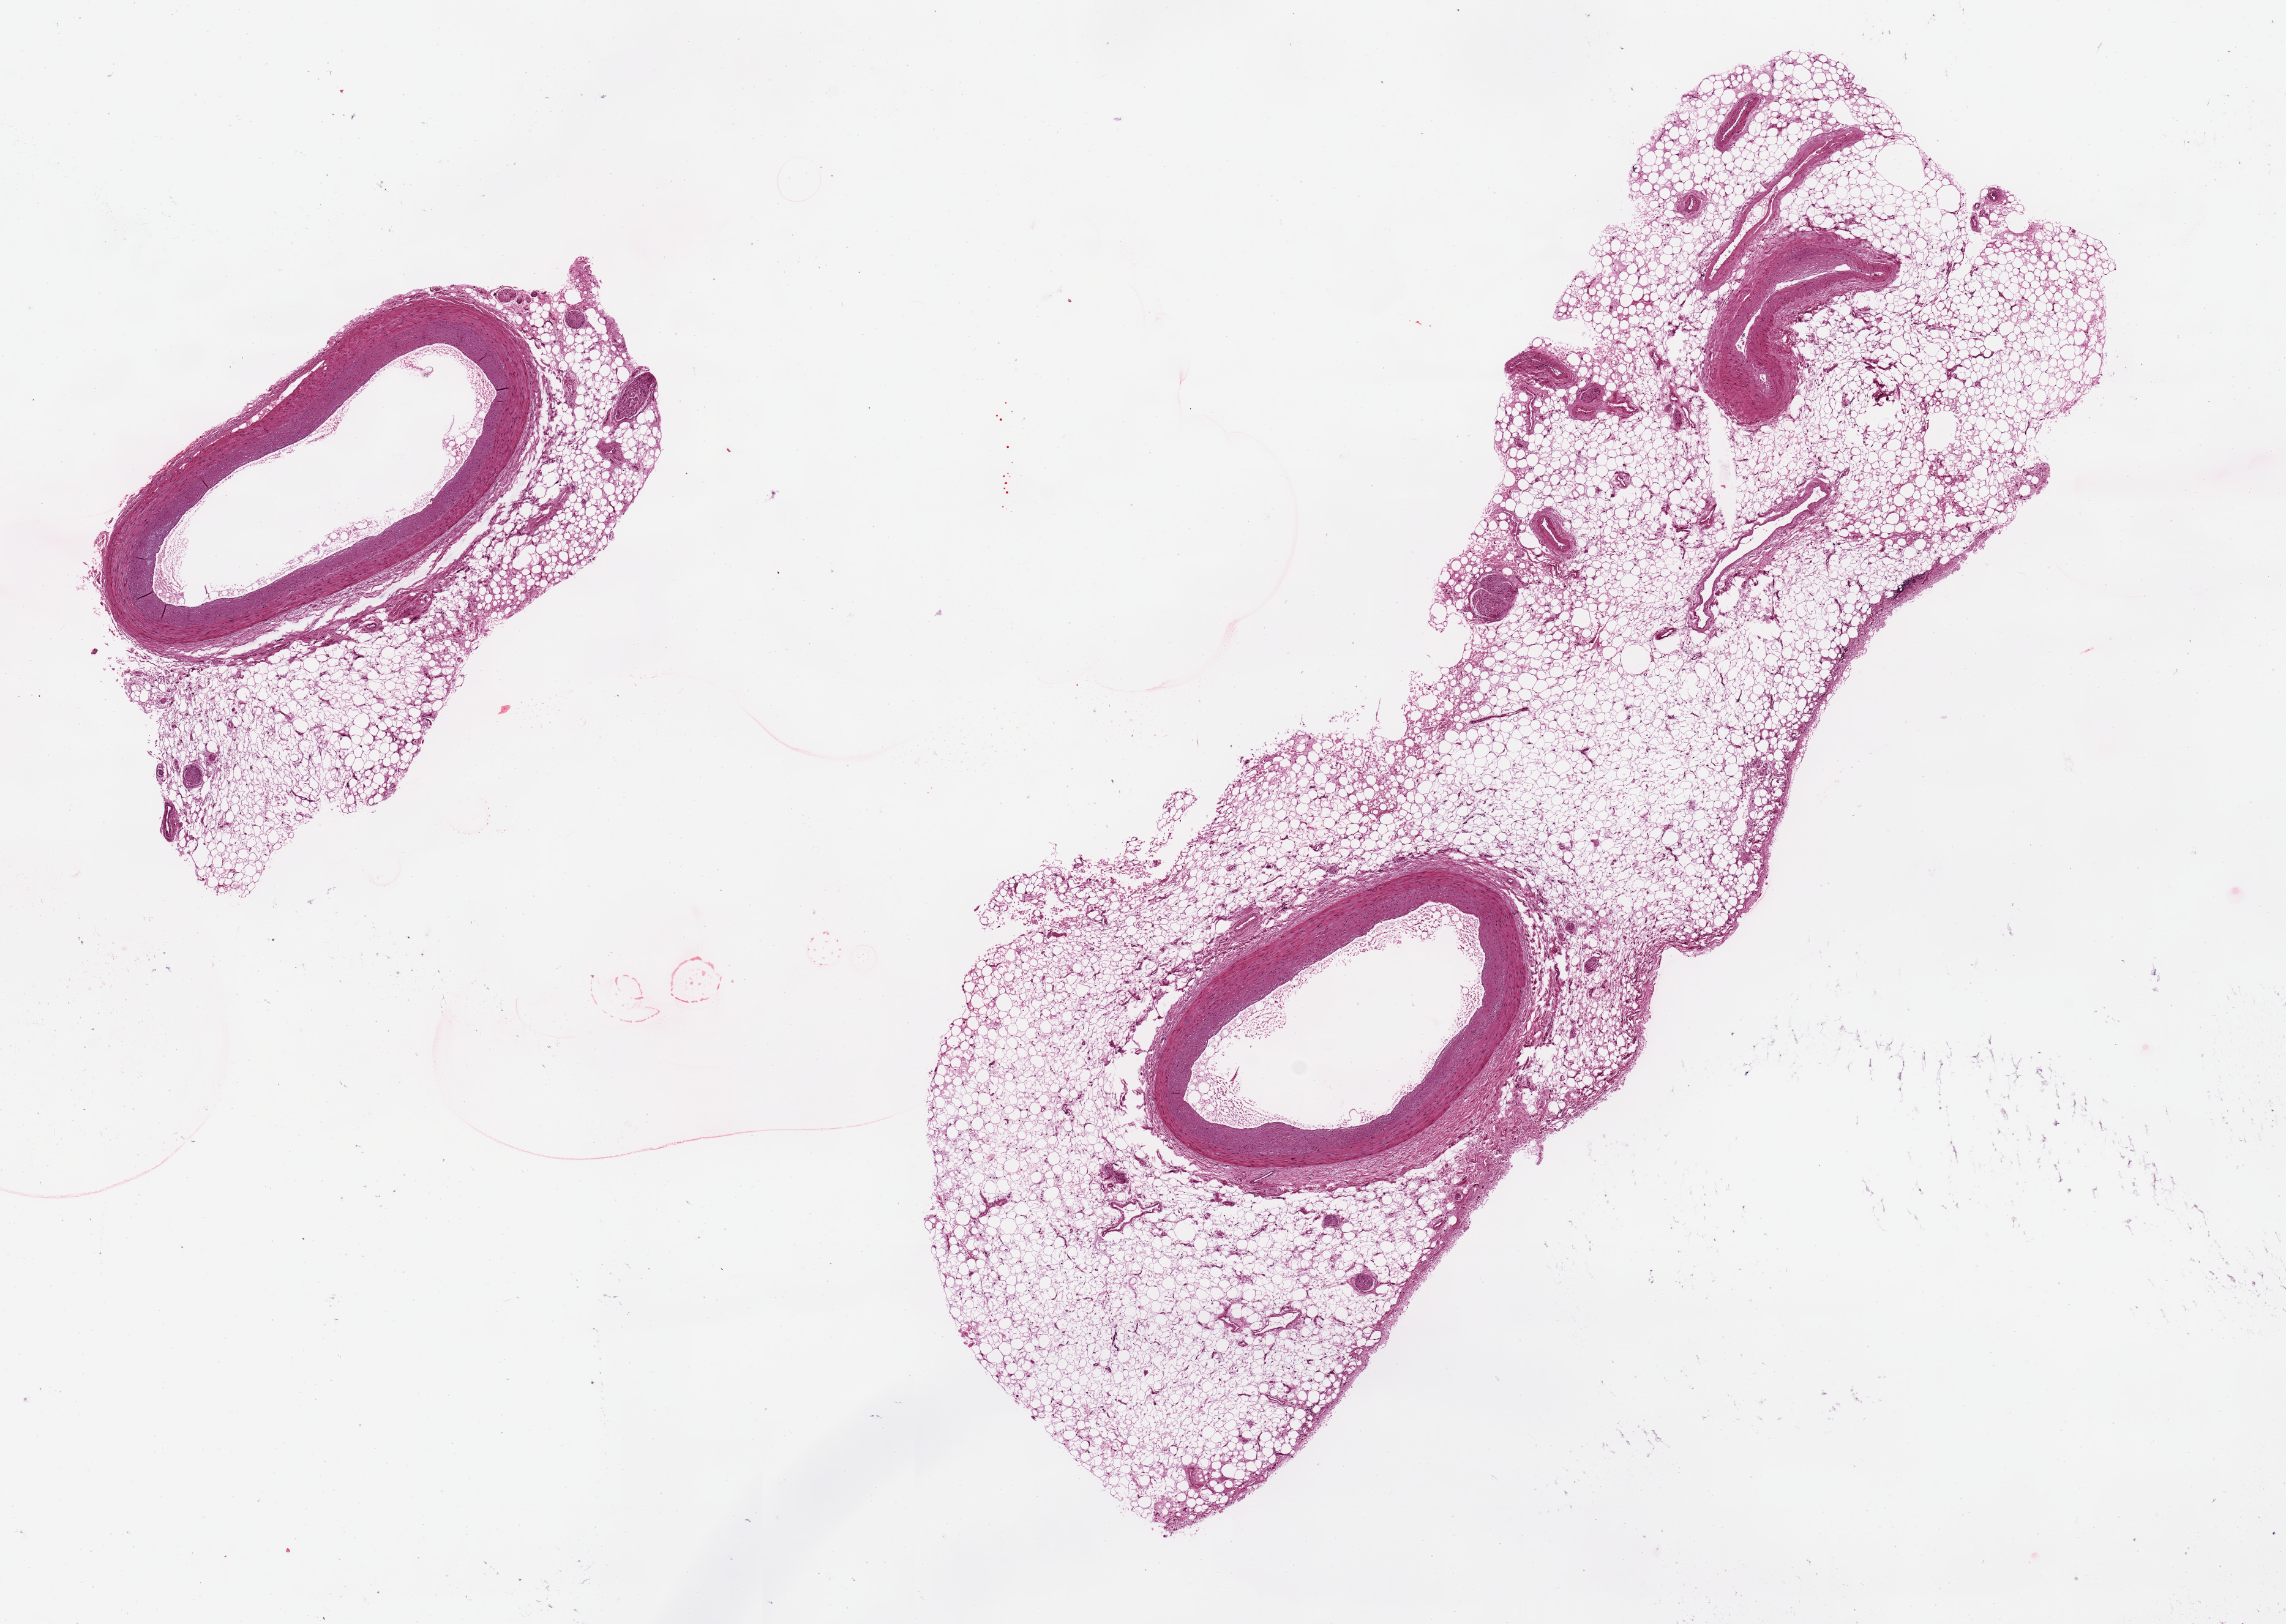
Digitized haematoxylin and eosin-stained section, shown as a low-resolution overview of the whole scanned area (about 14.8 x 10.5 mm, acquisition: 20x scan). PAXgene-fixed, paraffin-embedded tissue. Sampled site (target tissue): coronary artery. Tissue donor sample. Donor: female.
Reviewer comment on this tissue sample: One of 2 arteries is 2.5mm in diameter in 9 x 2.6mm fatty specimen.